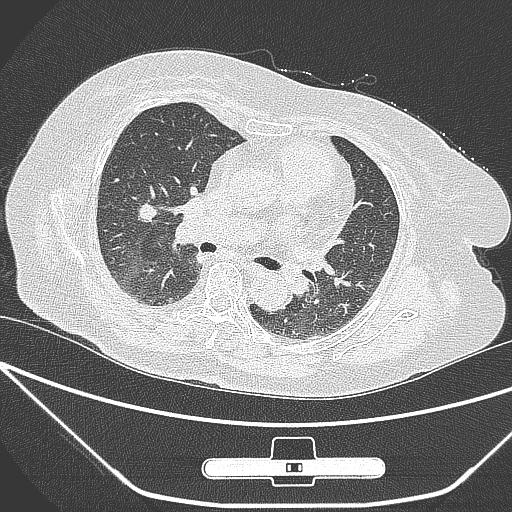
Chest CT, one axial slice; position 154 of 245 along the scan axis; 120 kVp; lung window (W 1500 / L -600 HU); 512 × 512 image matrix, field of view 365 × 365 mm. Female patient, age 65 years. From the clinical record (not read from this slice): clinical TNM (as recorded): T1c N0 M0; histopathological grade: G3.
Structures marked on this image (bounding box drawn by a radiologist):
- lung tumour (recorded histology: adenocarcinoma): box from (x=134, y=196) to (x=168, y=235) px